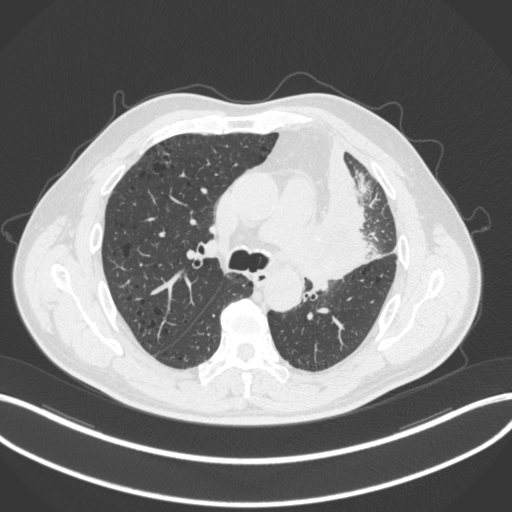
Chest CT, one axial slice. Position 182 of 286 along the scan axis. Reconstruction kernel B31f. Lung window (W 1500 / L -600 HU). 1 mm slice thickness. 512 × 512 image matrix, field of view 400 × 400 mm. Patient: male, 68 years. From the clinical record (not read from this slice): clinical TNM (as recorded): T3 N3 M1.
Annotated regions visible in this slice (rectangle marked by the reading radiologist):
- lung tumour (recorded histology: adenocarcinoma): bounding box (x1, y1, x2, y2) in pixels: (312, 200, 380, 287)